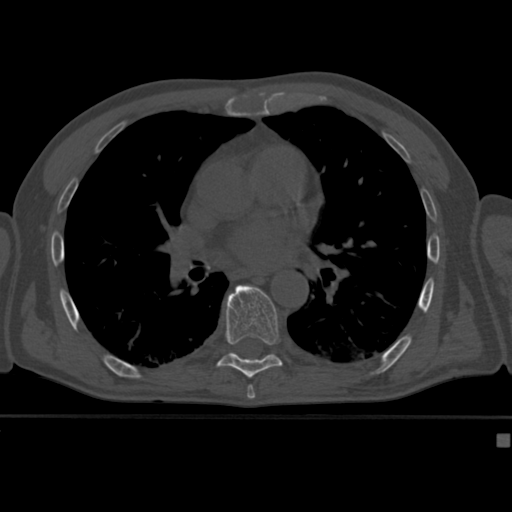
CT including the spine, one axial slice; reconstruction kernel Br40s; 120 kVp; bone window (W 1800 / L 400 HU); 512 × 512 image matrix. Male patient, age 64 years. Case-level facts recorded for this patient, not image findings: primary cancer: uterus; vertebrae with lytic lesions (as recorded): T1, T4, T5, T7, L5.
Annotated regions visible in this slice (semi-automatically segmented with operator editing):
- T8 vertebra: bounding box [x1, y1, x2, y2] px = [216, 285, 283, 378]
- T9 vertebra: [231, 352, 238, 356]